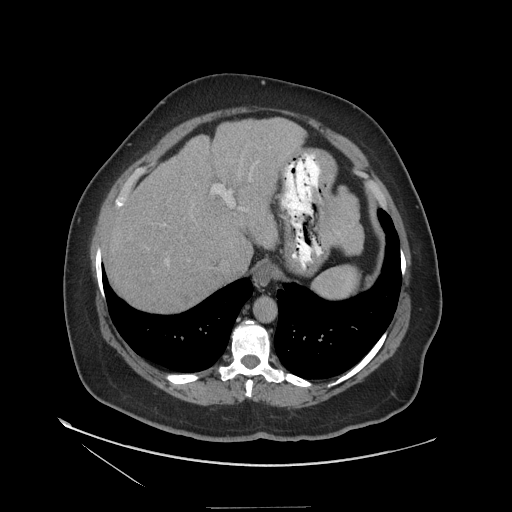
Contrast-enhanced abdominal CT (liver protocol), one axial slice; position 93 of 127 along the scan axis; reconstruction kernel STANDARD; 140 kVp; soft-tissue window (W 400 / L 40 HU); 2.5 mm slice thickness; 512 × 512 image matrix. From the clinical record (not read from this slice): diagnosis: hepatocellular carcinoma (patient treated with transarterial chemoembolisation; whether this scan precedes or follows treatment is not stated here); TNM stage (as recorded): Stage-II; Child-Pugh class: A; tumour nodularity: multinodular; tumour size: 3 cm.
Structures marked on this image (semi-automatic segmentation, software-assisted and operator-edited):
- abdominal aorta: box from (x=253, y=297) to (x=275, y=323) px
- liver parenchyma outside the tumour (the mass and vessels are separate outlines, so this box may not span the whole liver): (x=104, y=118)–(x=304, y=312)
- mass: (x=125, y=240)–(x=138, y=249)
- liver vessels: (x=117, y=185)–(x=232, y=207)